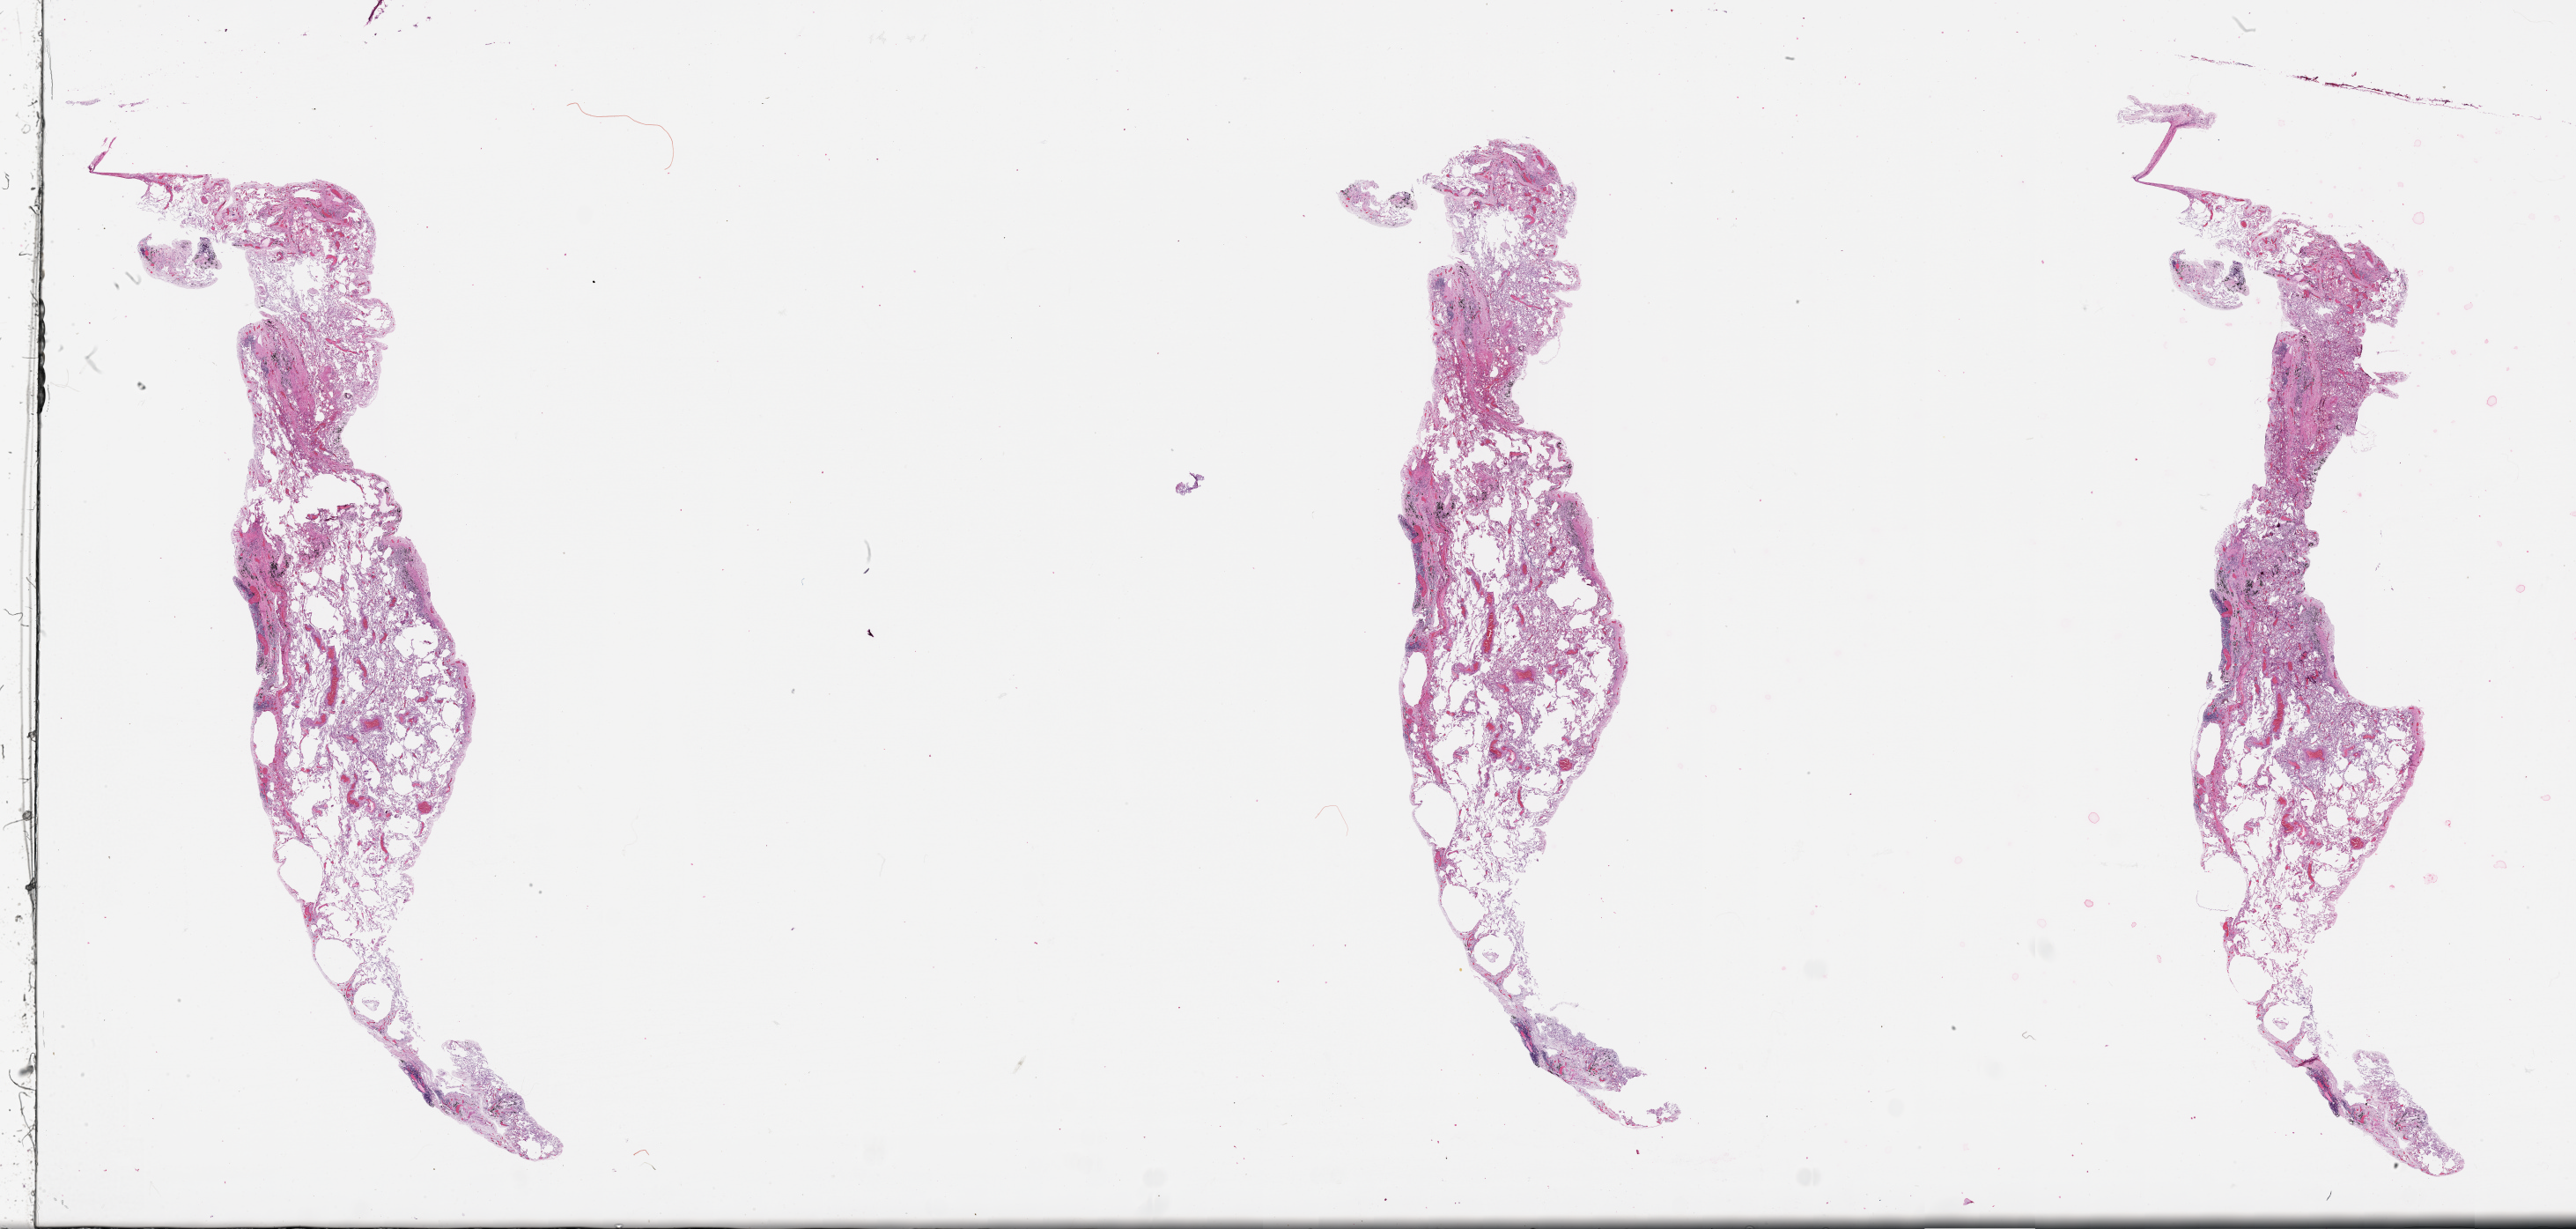
Hematoxylin and eosin (H&E) stained whole-slide image, whole scanned area (about 47.1 x 22.5 mm) shown as a low-resolution overview. Lung, tissue type not recorded.
Patient diagnosis (cohort enrolment): lung adenocarcinoma (lung).